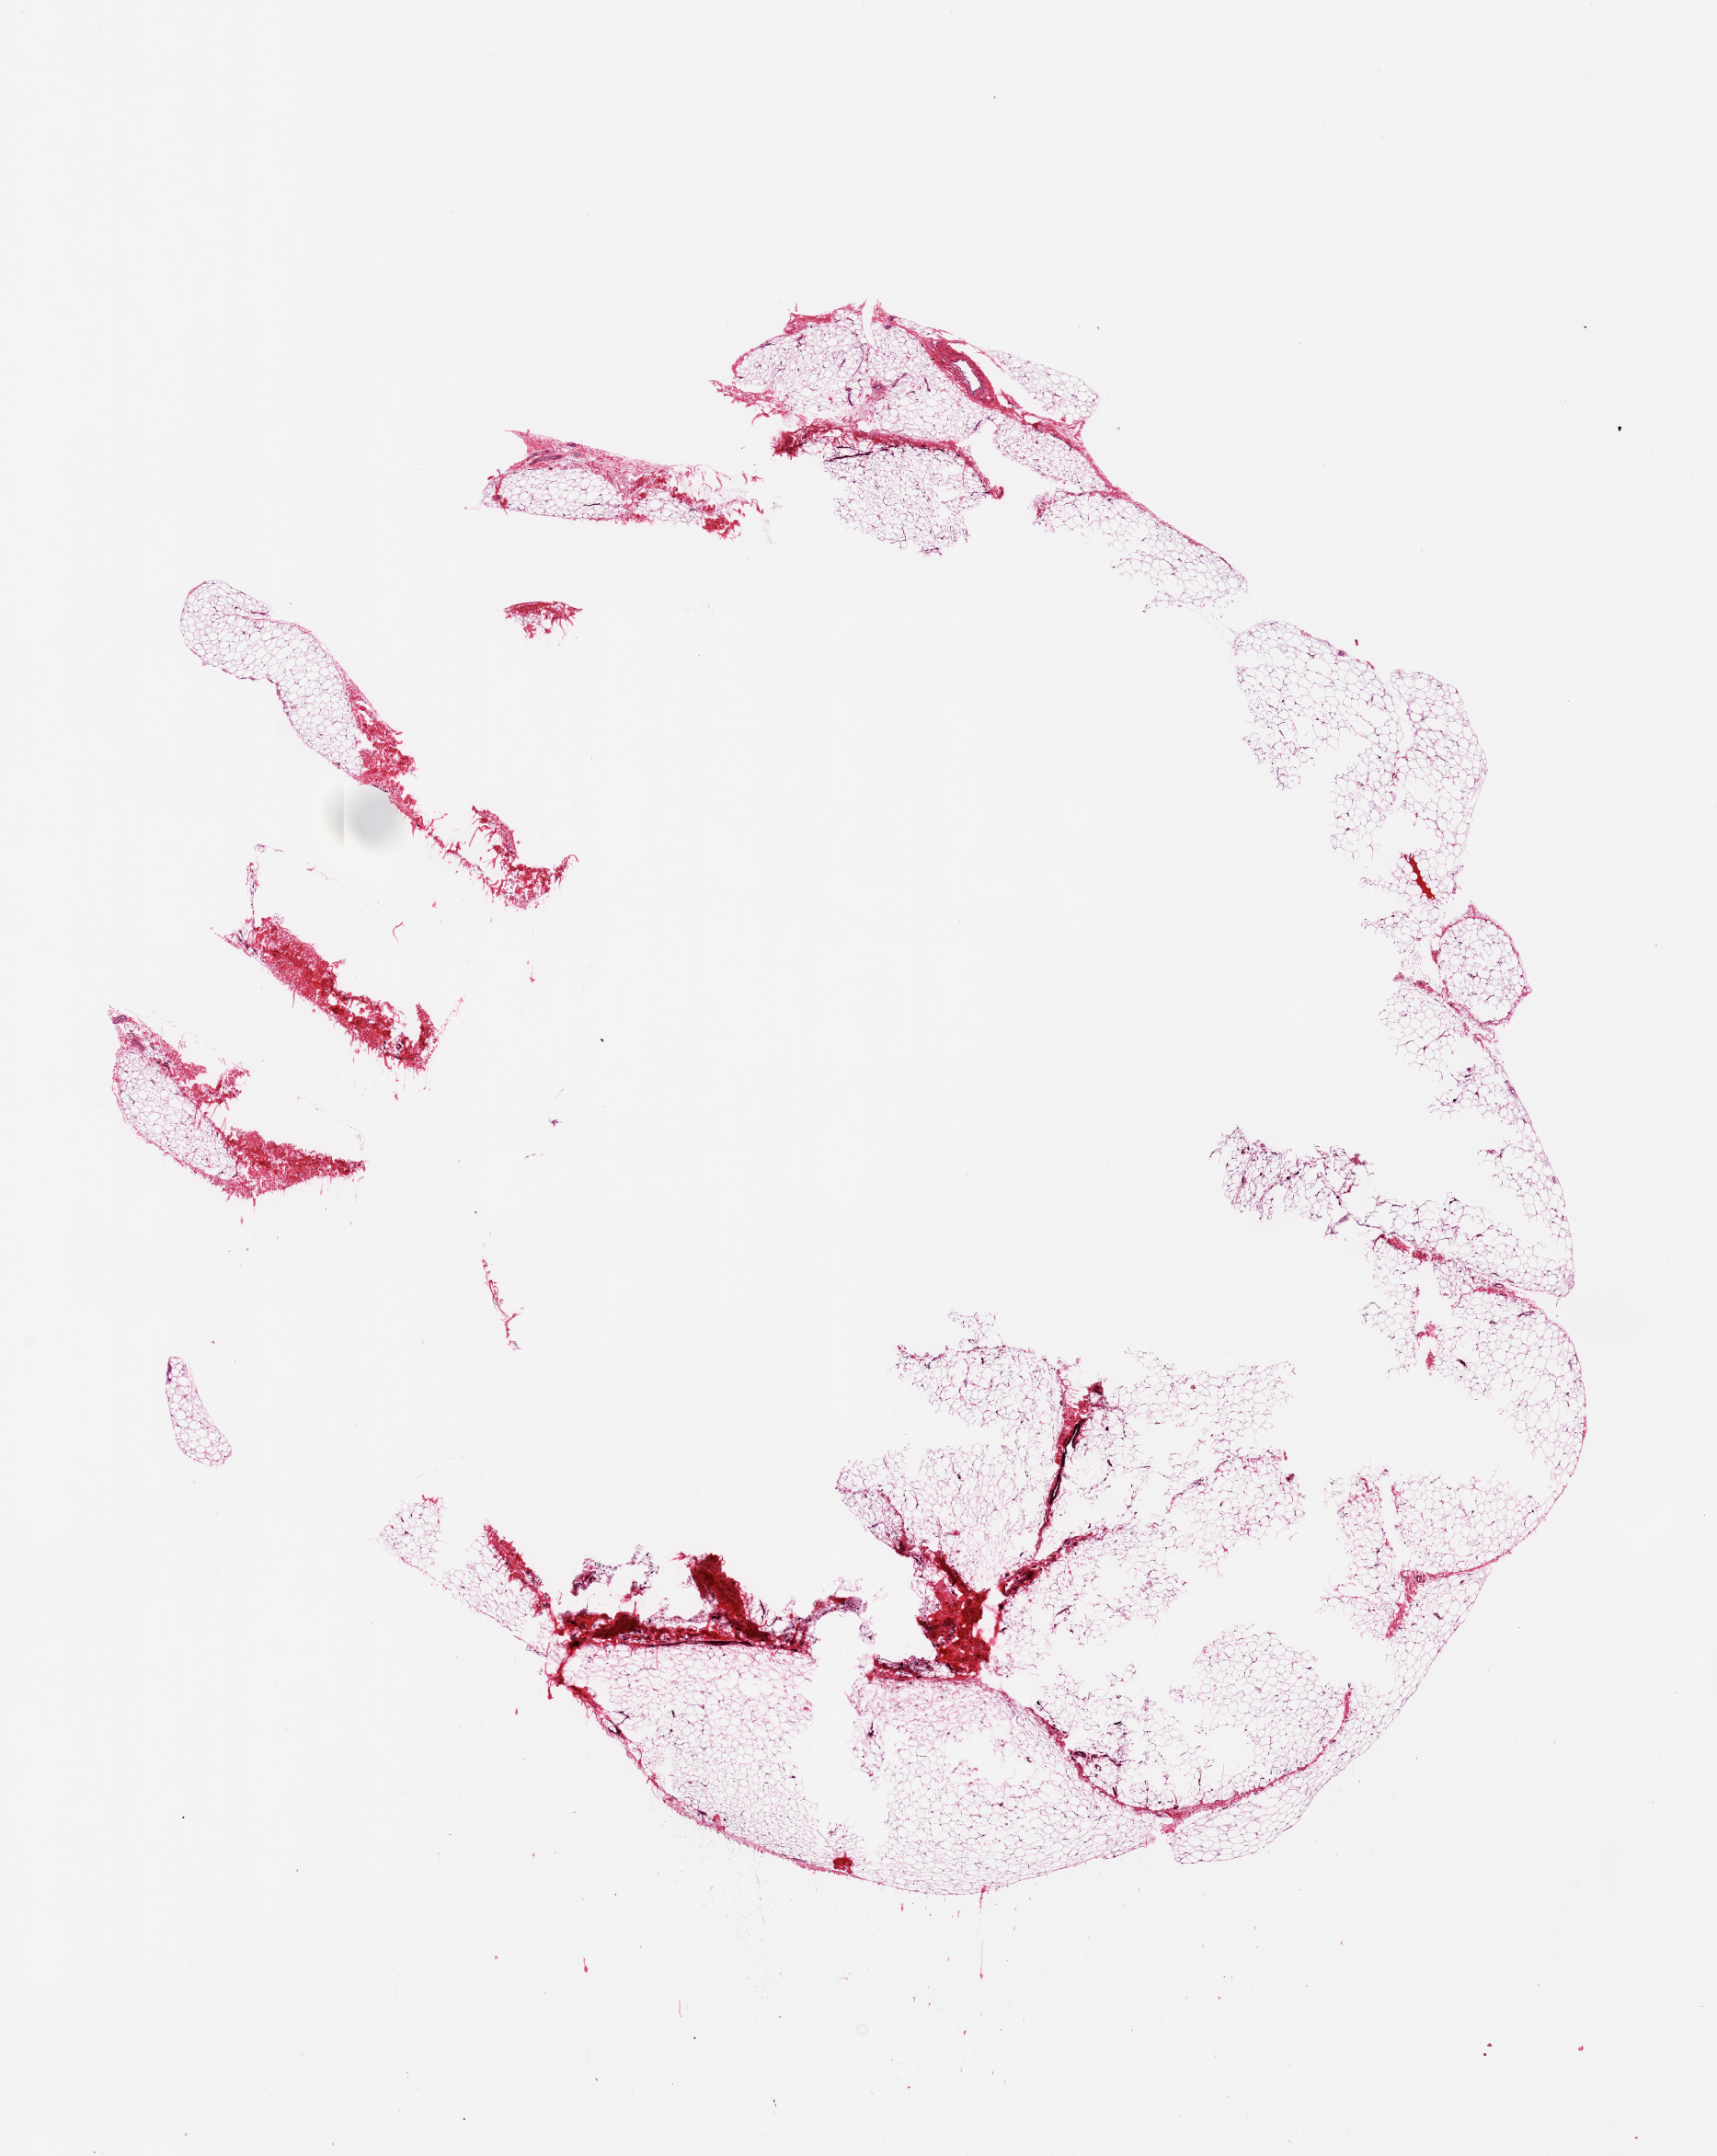
Digitized H&E-stained section, shown as a low-resolution overview of the whole scanned area (about 14.8 x 18.5 mm). PAXgene-fixed, paraffin-embedded tissue. Section of adipose tissue (target tissue). Tissue donor sample. Male donor.
Pathologist's review note for this sample: (80% centrally unfixed); 12x13.6mm aliquot: too large.